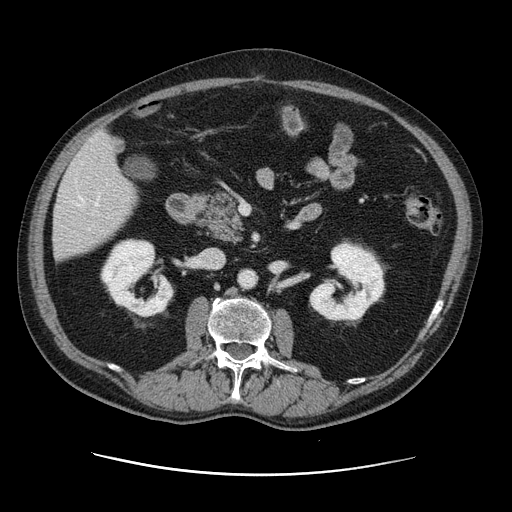
Contrast-enhanced abdominal CT, one axial slice. Position 49 of 141 along the scan axis. Intravenous contrast given. Soft-tissue window (W 400 / L 40 HU). 512 × 512 image matrix. Male patient, age 72 years. Case-level facts recorded for this patient, not image findings: diagnosis: colorectal cancer liver metastases, imaged before liver resection; multiple liver metastases: yes; largest metastasis: 5.4 cm; disease in both lobes: yes.
Outlined on this slice (outlined manually by an expert reader):
- hepatic veins: bounding box [x1, y1, x2, y2] px = [74, 196, 100, 230]
- liver: [54, 134, 137, 259]
- planned liver remnant (the part of the liver to remain after resection): [54, 164, 137, 260]